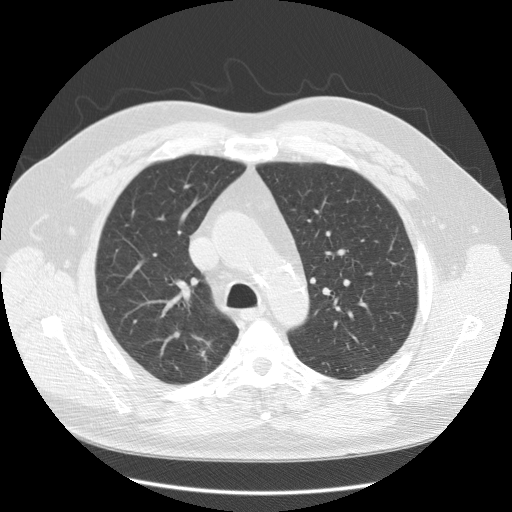
Low-dose screening chest CT, one axial slice; position 90 of 125 along the scan axis; 120 kVp; lung window (W 1500 / L -600 HU); 2.5 mm slice thickness; 512 × 512 image matrix, field of view 380 × 380 mm.
Annotated regions visible in this slice (manually delineated by an expert):
- lesion 1 (tumor, upper lobe of right lung): box from (x=200, y=350) to (x=207, y=361) px